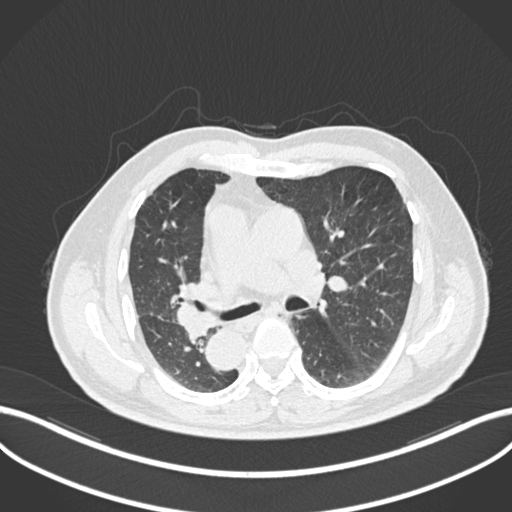
Chest CT, one axial slice; slice 131 of 206 in the series (ordered by position); 120 kVp; lung window (W 1500 / L -600 HU); 1 mm slice thickness; 512 × 512 image matrix, field of view 400 × 400 mm. Patient: male, 67 years. From the clinical record (not read from this slice): clinical TNM (as recorded): T2a N0 M0.
Outlined on this slice (rectangle marked by the reading radiologist):
- lung tumour (recorded histology: squamous cell carcinoma): bounding box <170,282,221,341> (left, top, right, bottom; pixels)